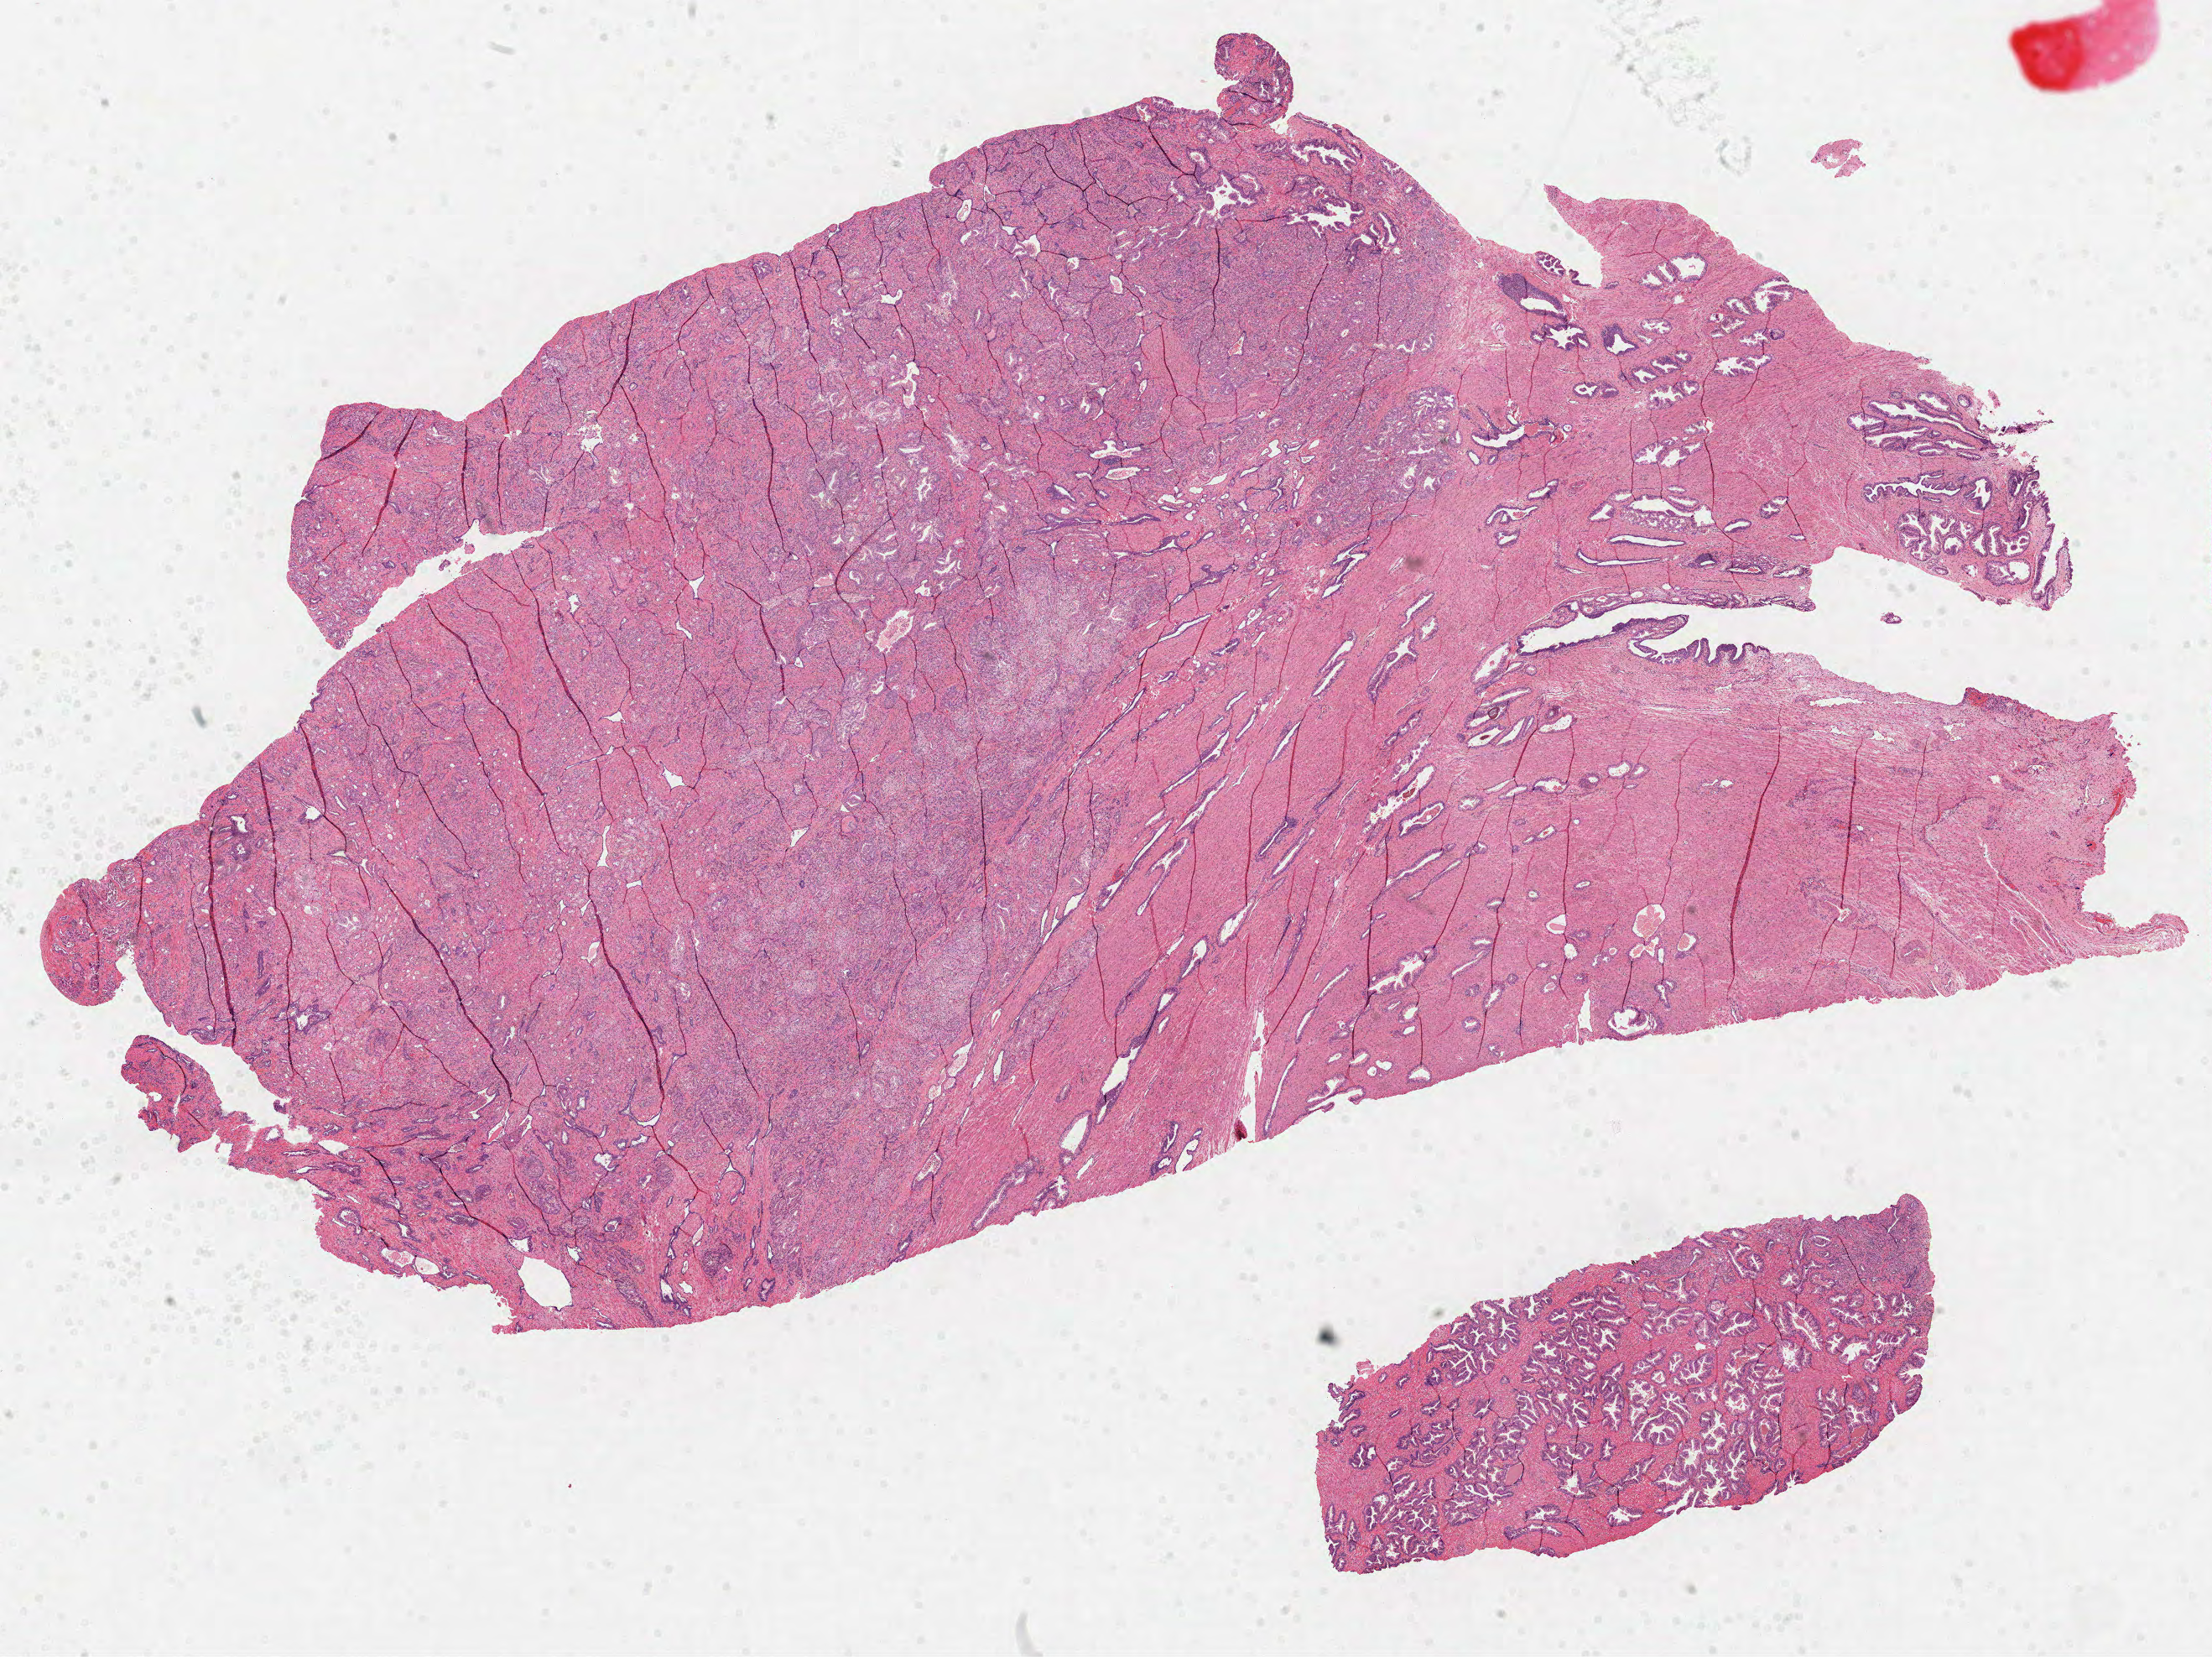
Whole-slide histology image, H&E — low-resolution overview of the scanned area, about 21.3 x 15.9 mm (from a 40x scan). Formalin-fixed paraffin-embedded (FFPE) diagnostic section. Prostate, primary tumour sample. Male, age 49 years at initial diagnosis. Gleason score: 7 (3+4).
Histologic diagnosis: Acinar cell carcinoma (prostate gland). Laterality: bilateral.